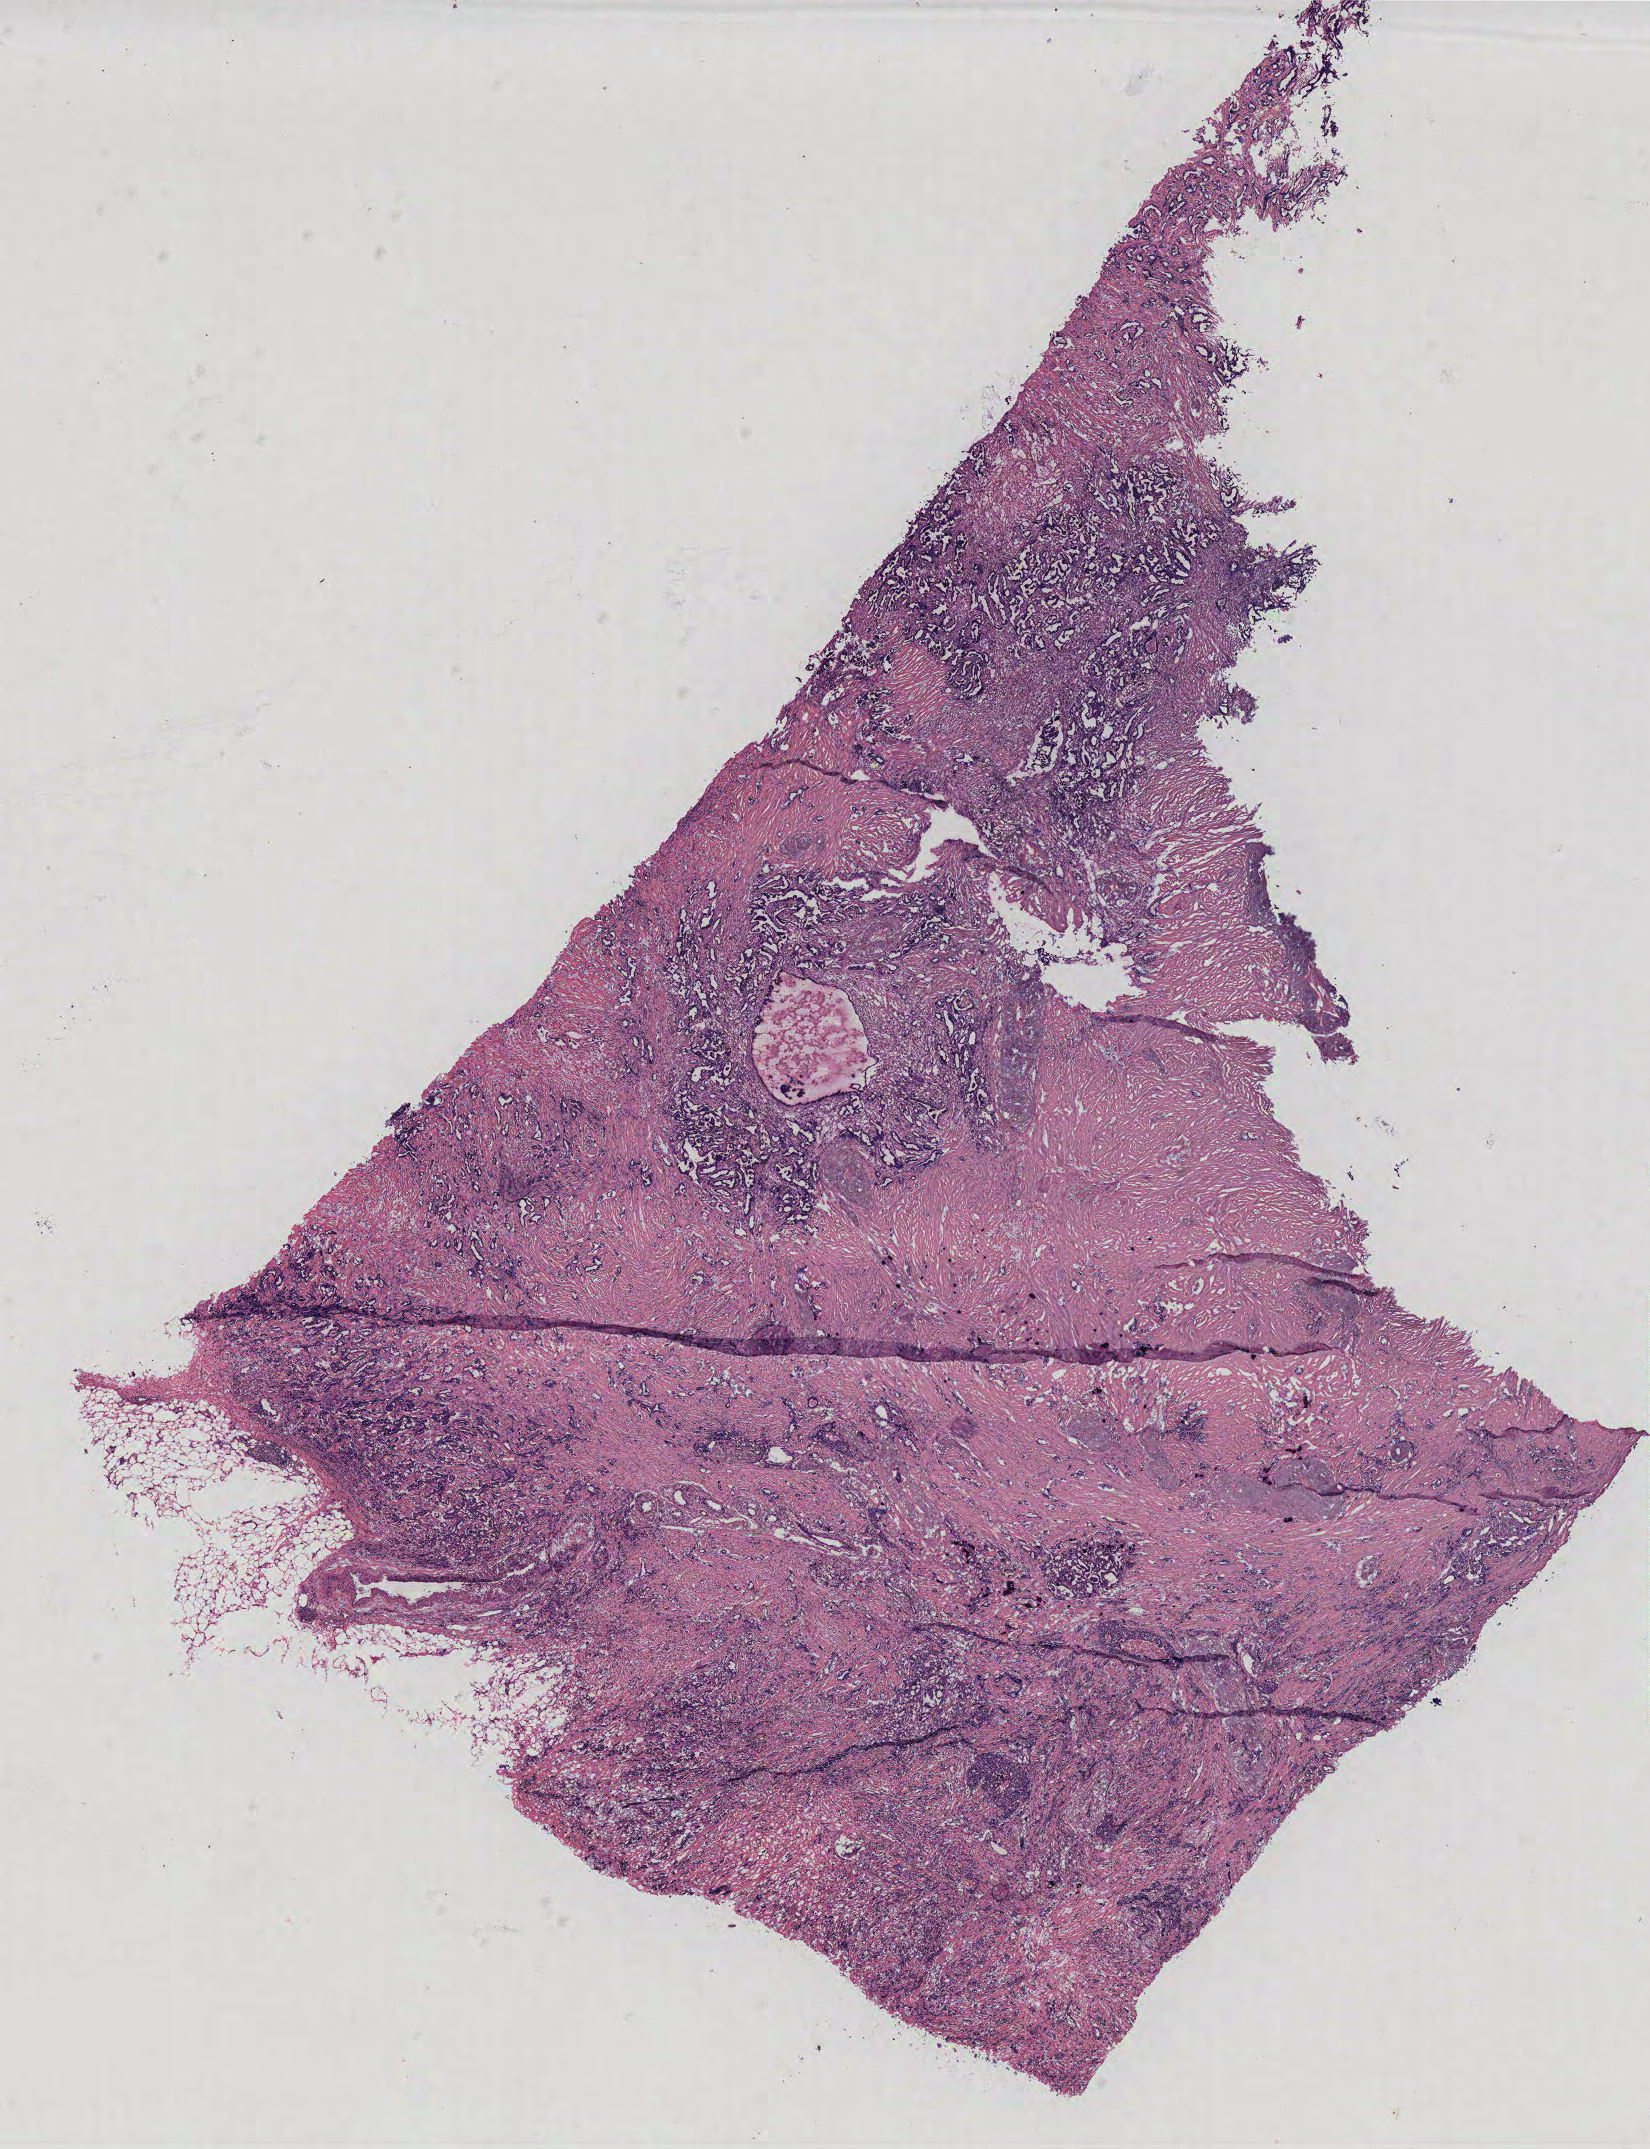
Digitized H&E-stained tissue section (whole slide), low-resolution overview of the scanned area, about 13.2 x 17.2 mm (acquisition: 40x scan). Breast, tissue type not recorded. Patient: female, age 59 years.
Patient diagnosis: Infiltrating lobular carcinoma, NOS.